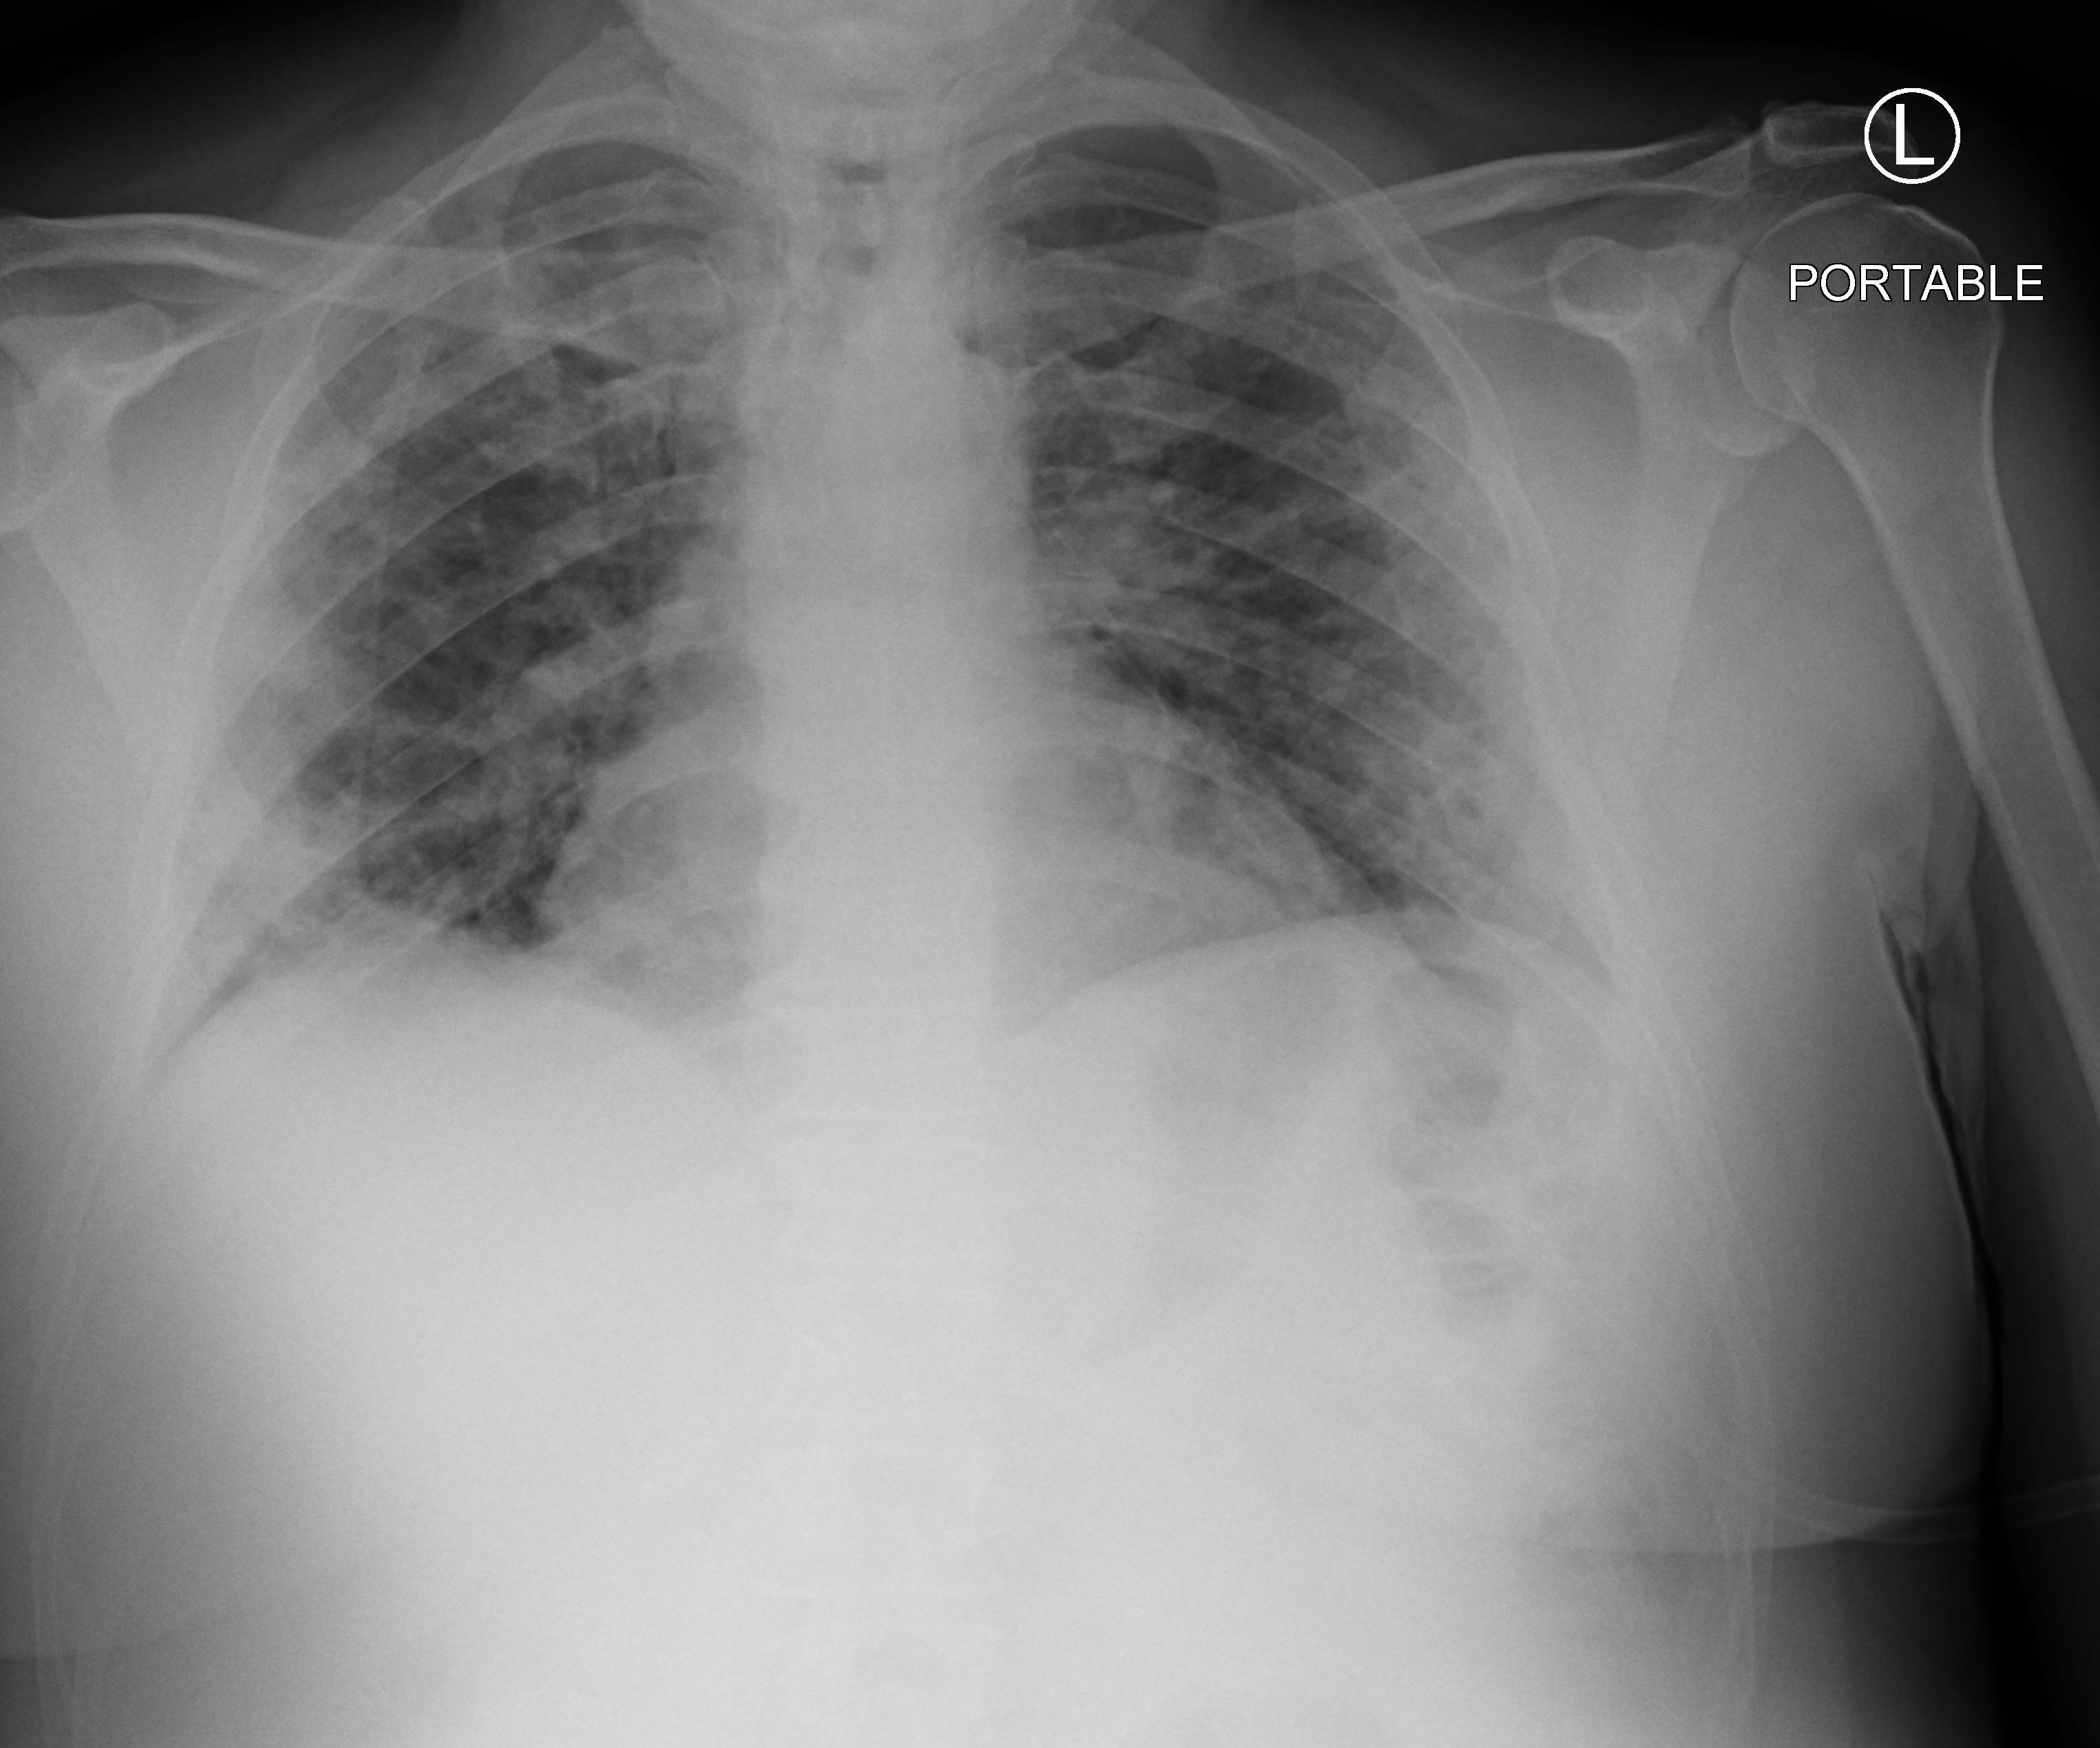
Bedside chest radiograph (computed radiography). Patient hospitalised with COVID-19; male, aged 18–59 years.
Admission-level facts for this patient (not findings on this image; timing relative to this image not recorded): mechanically ventilated during this hospital stay: no; admitted to intensive care during this hospital stay: yes; smoking status (admission record): never.